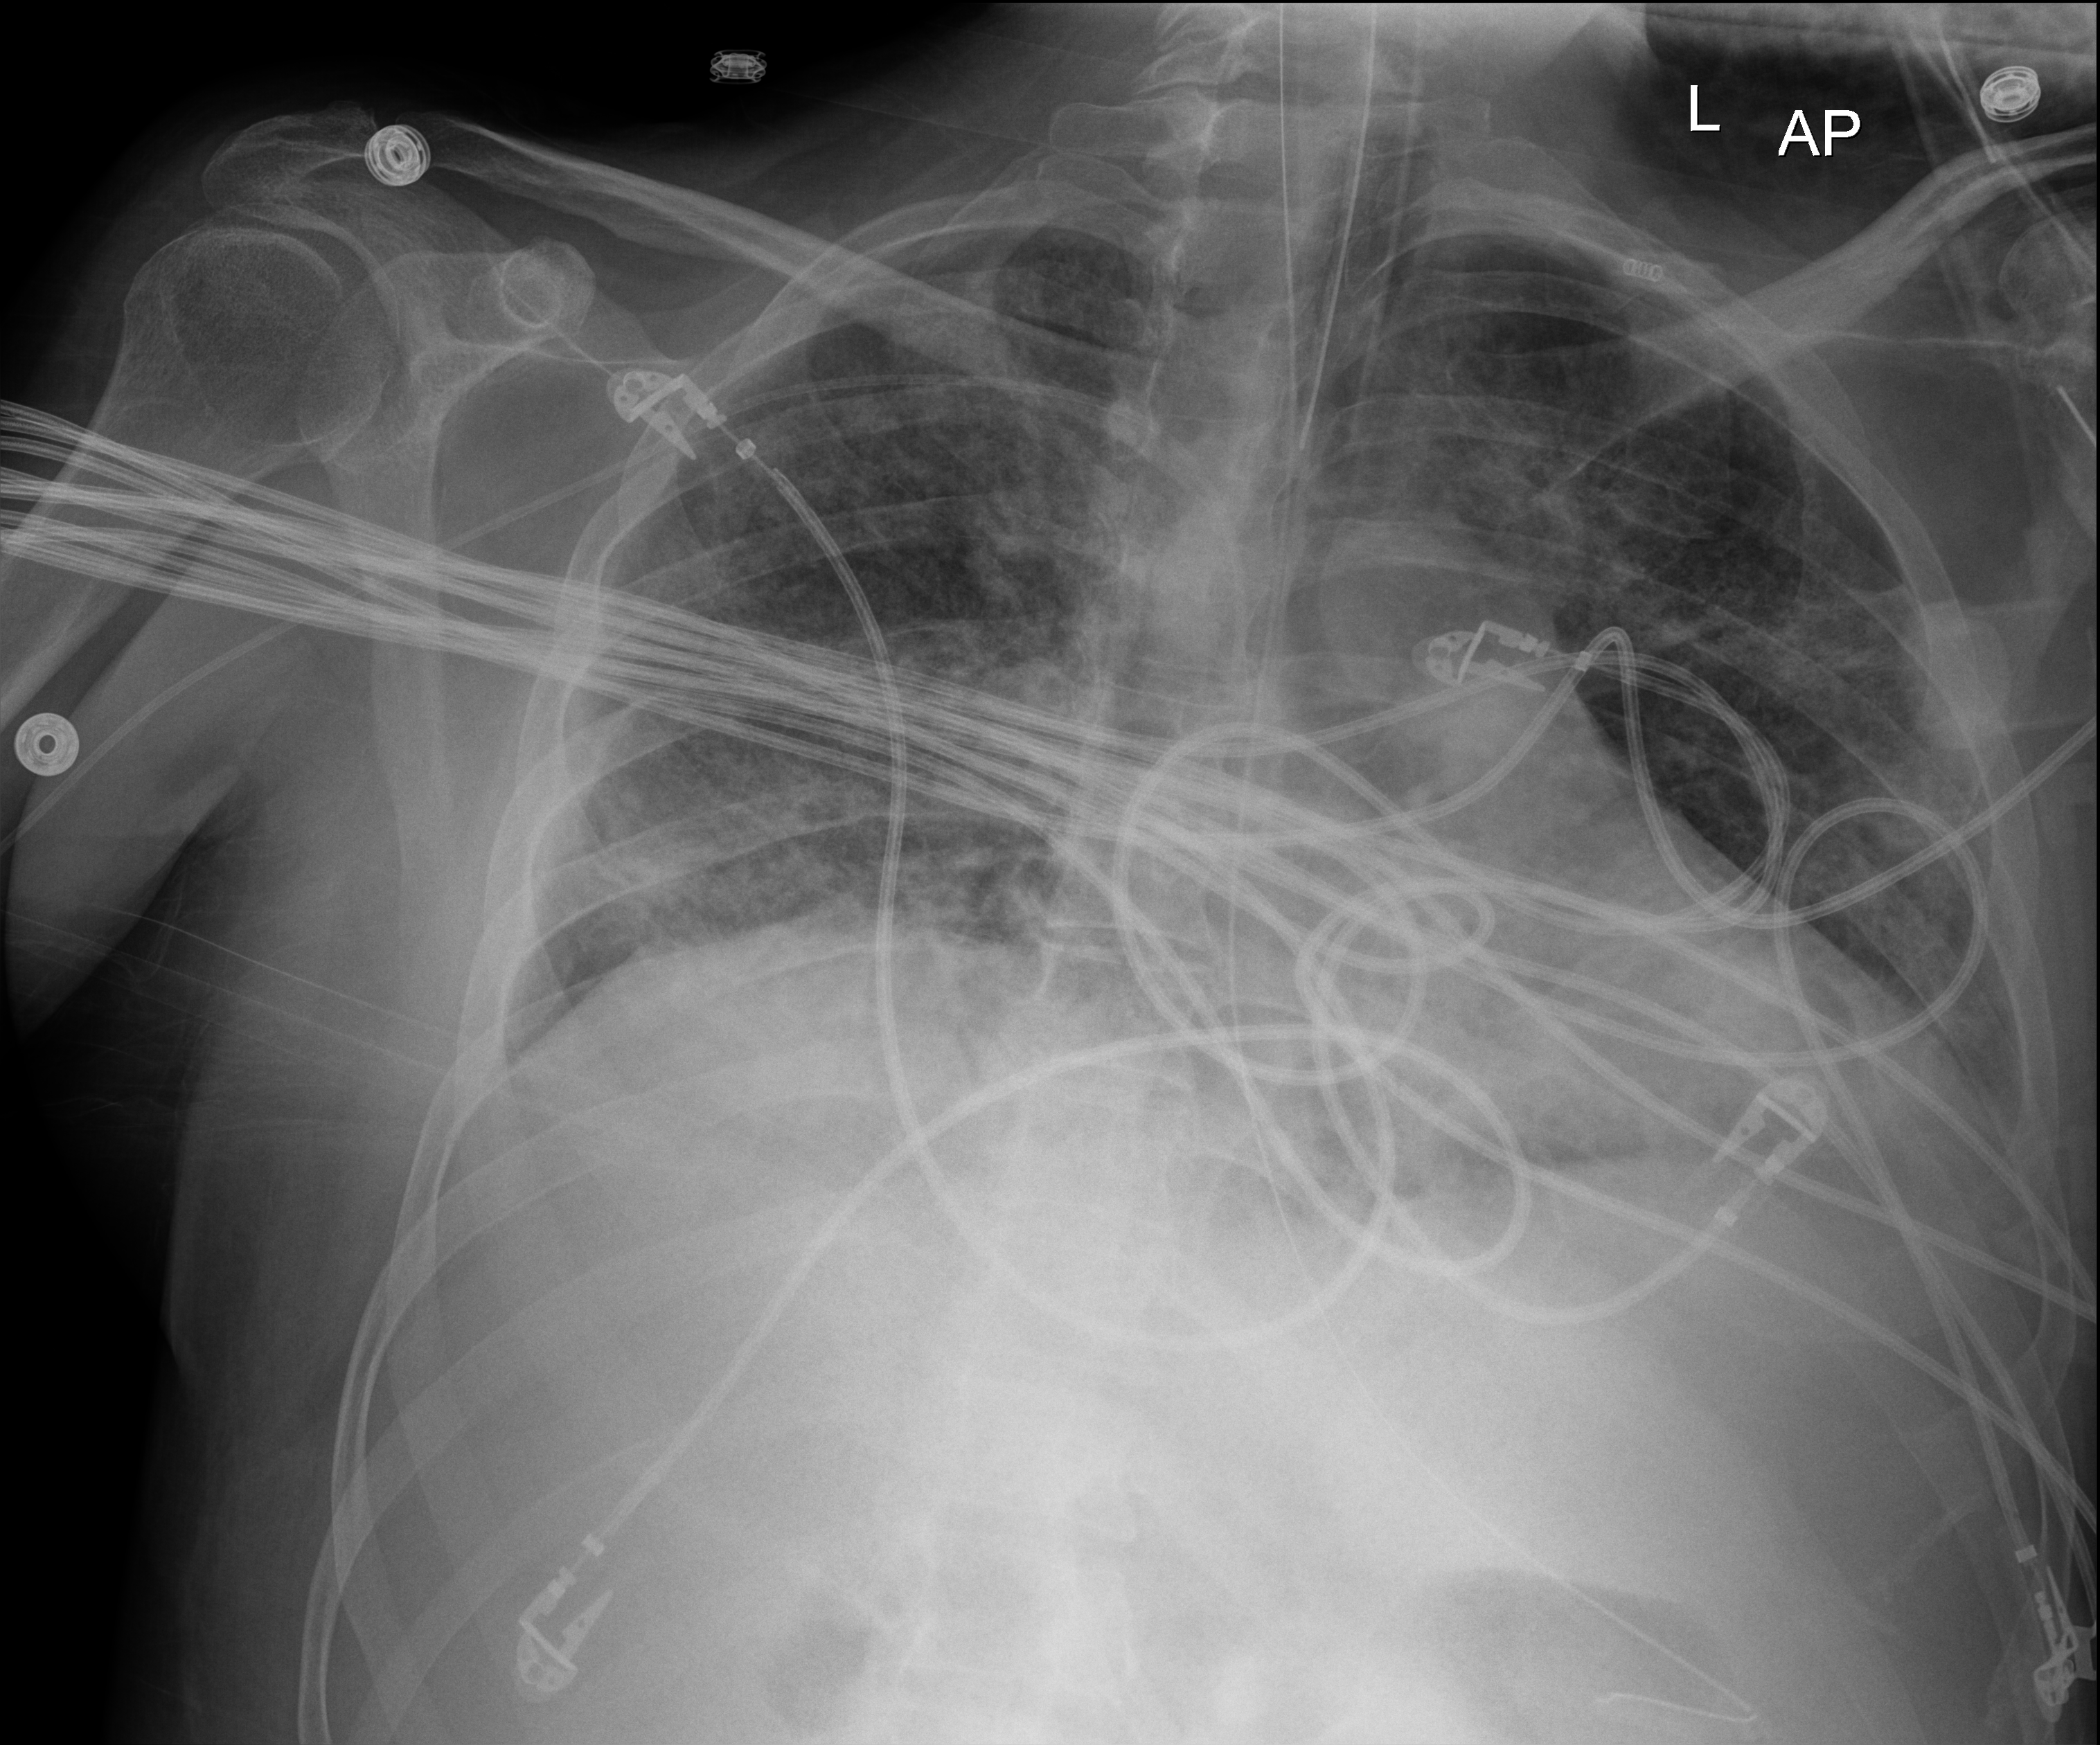
Portable chest radiograph; anteroposterior (AP) projection. Male patient hospitalised with COVID-19, age 18–59 years.
Hospital-stay facts (about this admission, not read from this image; timing relative to this image not recorded):
- length of hospital stay: 48 days
- COPD (admission record): no
- admitted to intensive care during this hospital stay: yes